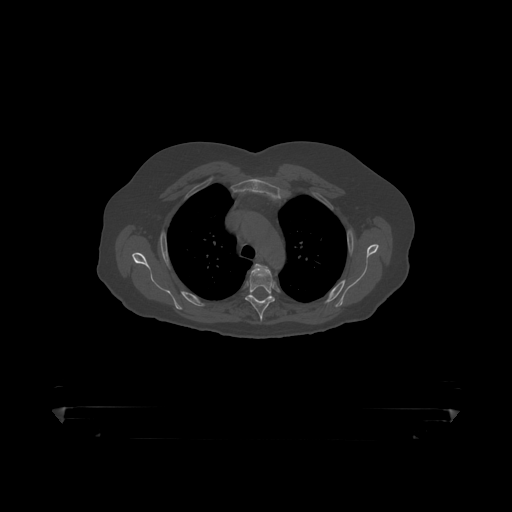
CT including the spine, one axial slice; 120 kVp; bone window (W 1800 / L 400 HU); 1.25 mm slice thickness; 512 × 512 image matrix, field of view 650 × 650 mm. Male patient, age 60 years. From the clinical record (not read from this slice): primary cancer: prostate.
Structures marked on this image (semi-automatic segmentation, software-assisted and operator-edited):
- T4 vertebra: bounding box (x1, y1, x2, y2) in pixels: (246, 264, 276, 319)